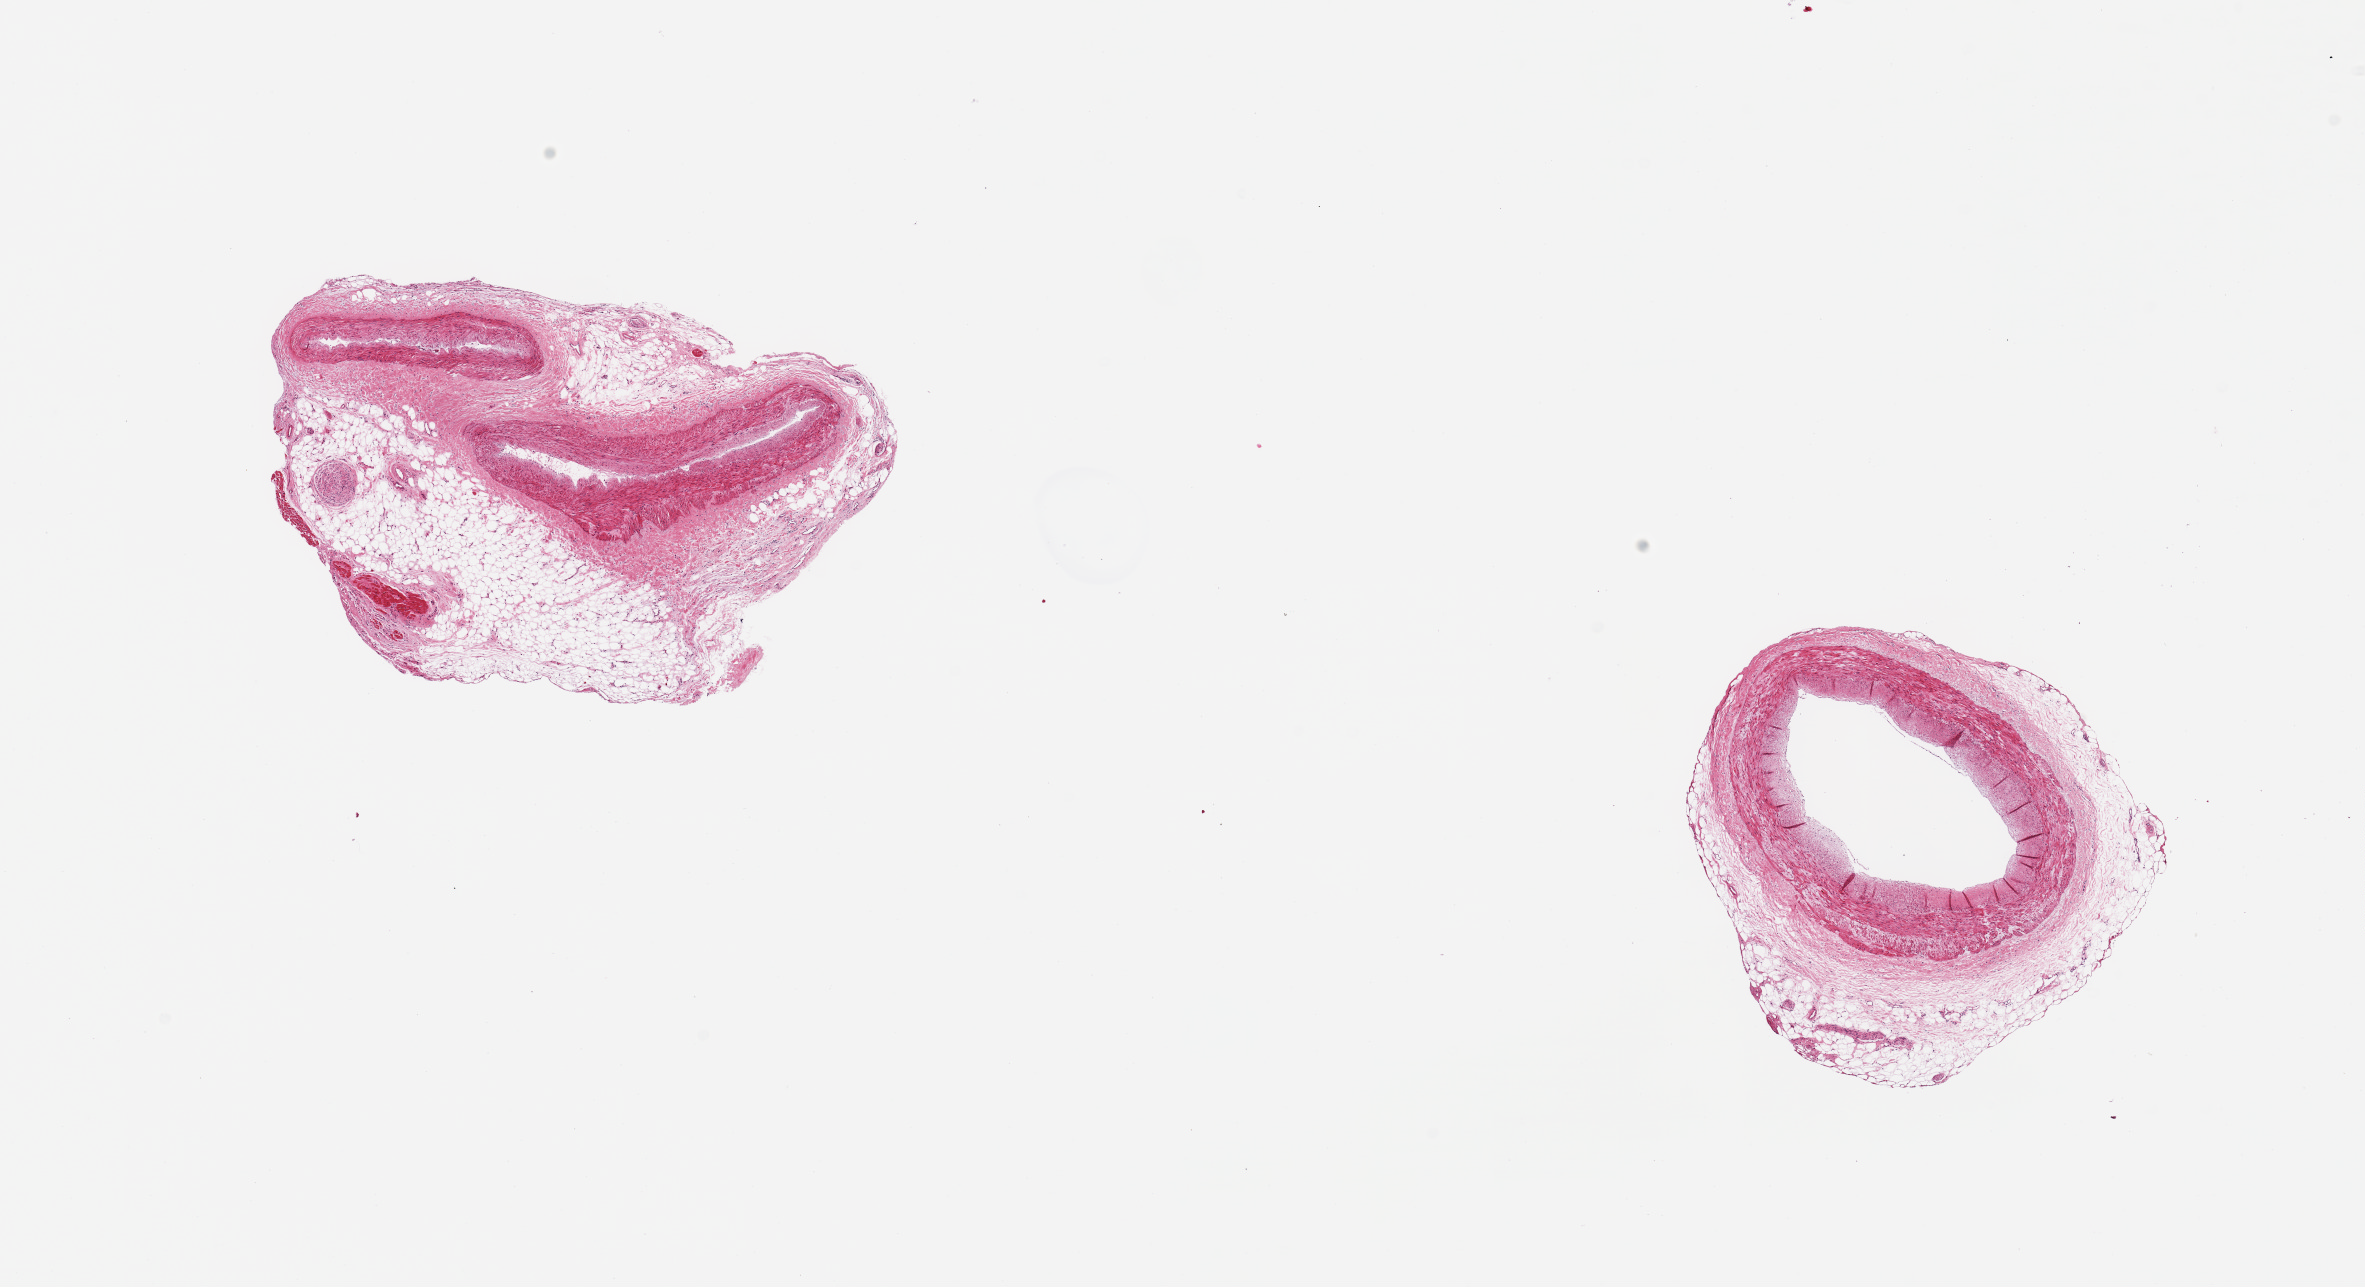
Haematoxylin and eosin whole-slide image, brightfield — low-resolution overview of the scanned area, about 18.7 x 10.2 mm (from a 20x scan), PAXgene-fixed, paraffin-embedded tissue, sampled site (target tissue): coronary artery, donor tissue sample. Donor sex: female.
• reviewer comment on this tissue sample: 2 pieces; early atherosis and up to 1.6mm attached adventitia and fat